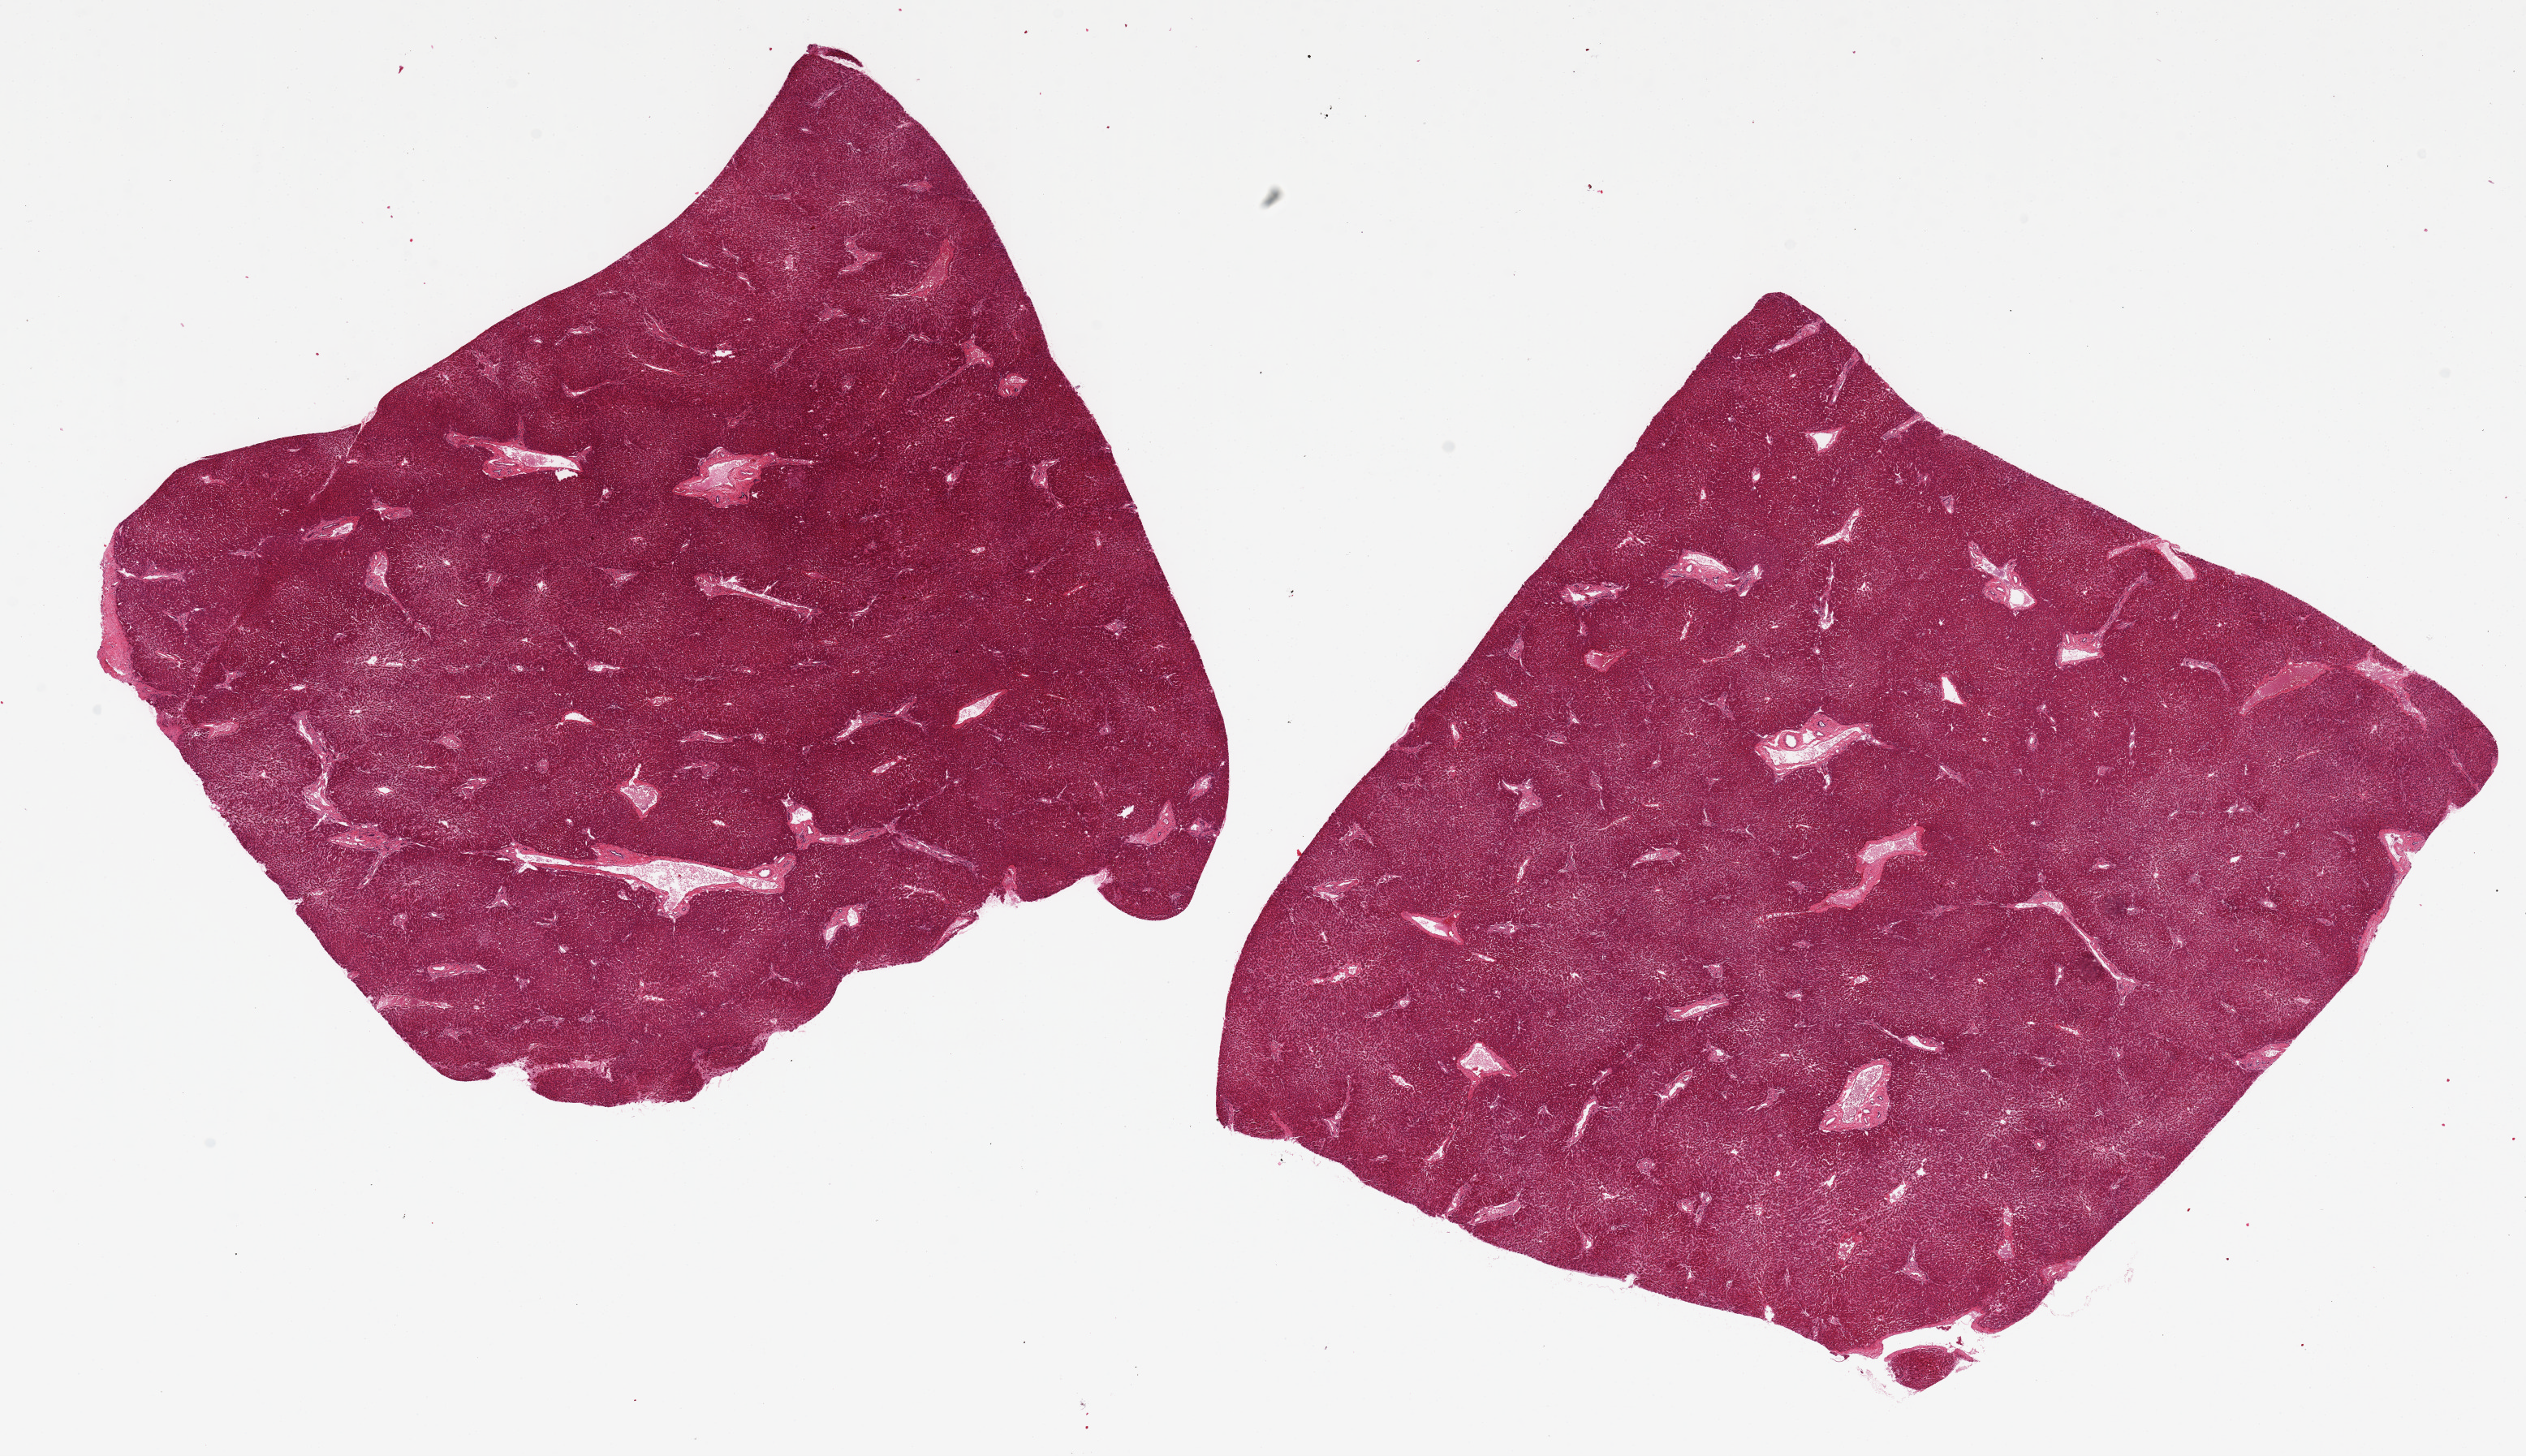
H&E whole-slide image, low-resolution overview of the scanned area, about 24.6 x 14.2 mm (acquisition: 20x scan); PAXgene-fixed, paraffin-embedded tissue; sampled site (target tissue): liver; tissue donor sample. Male donor.
Reviewer comment on this tissue sample: 2 pieces ~9x8mm; central pallor; no fibrosis or inflammation.